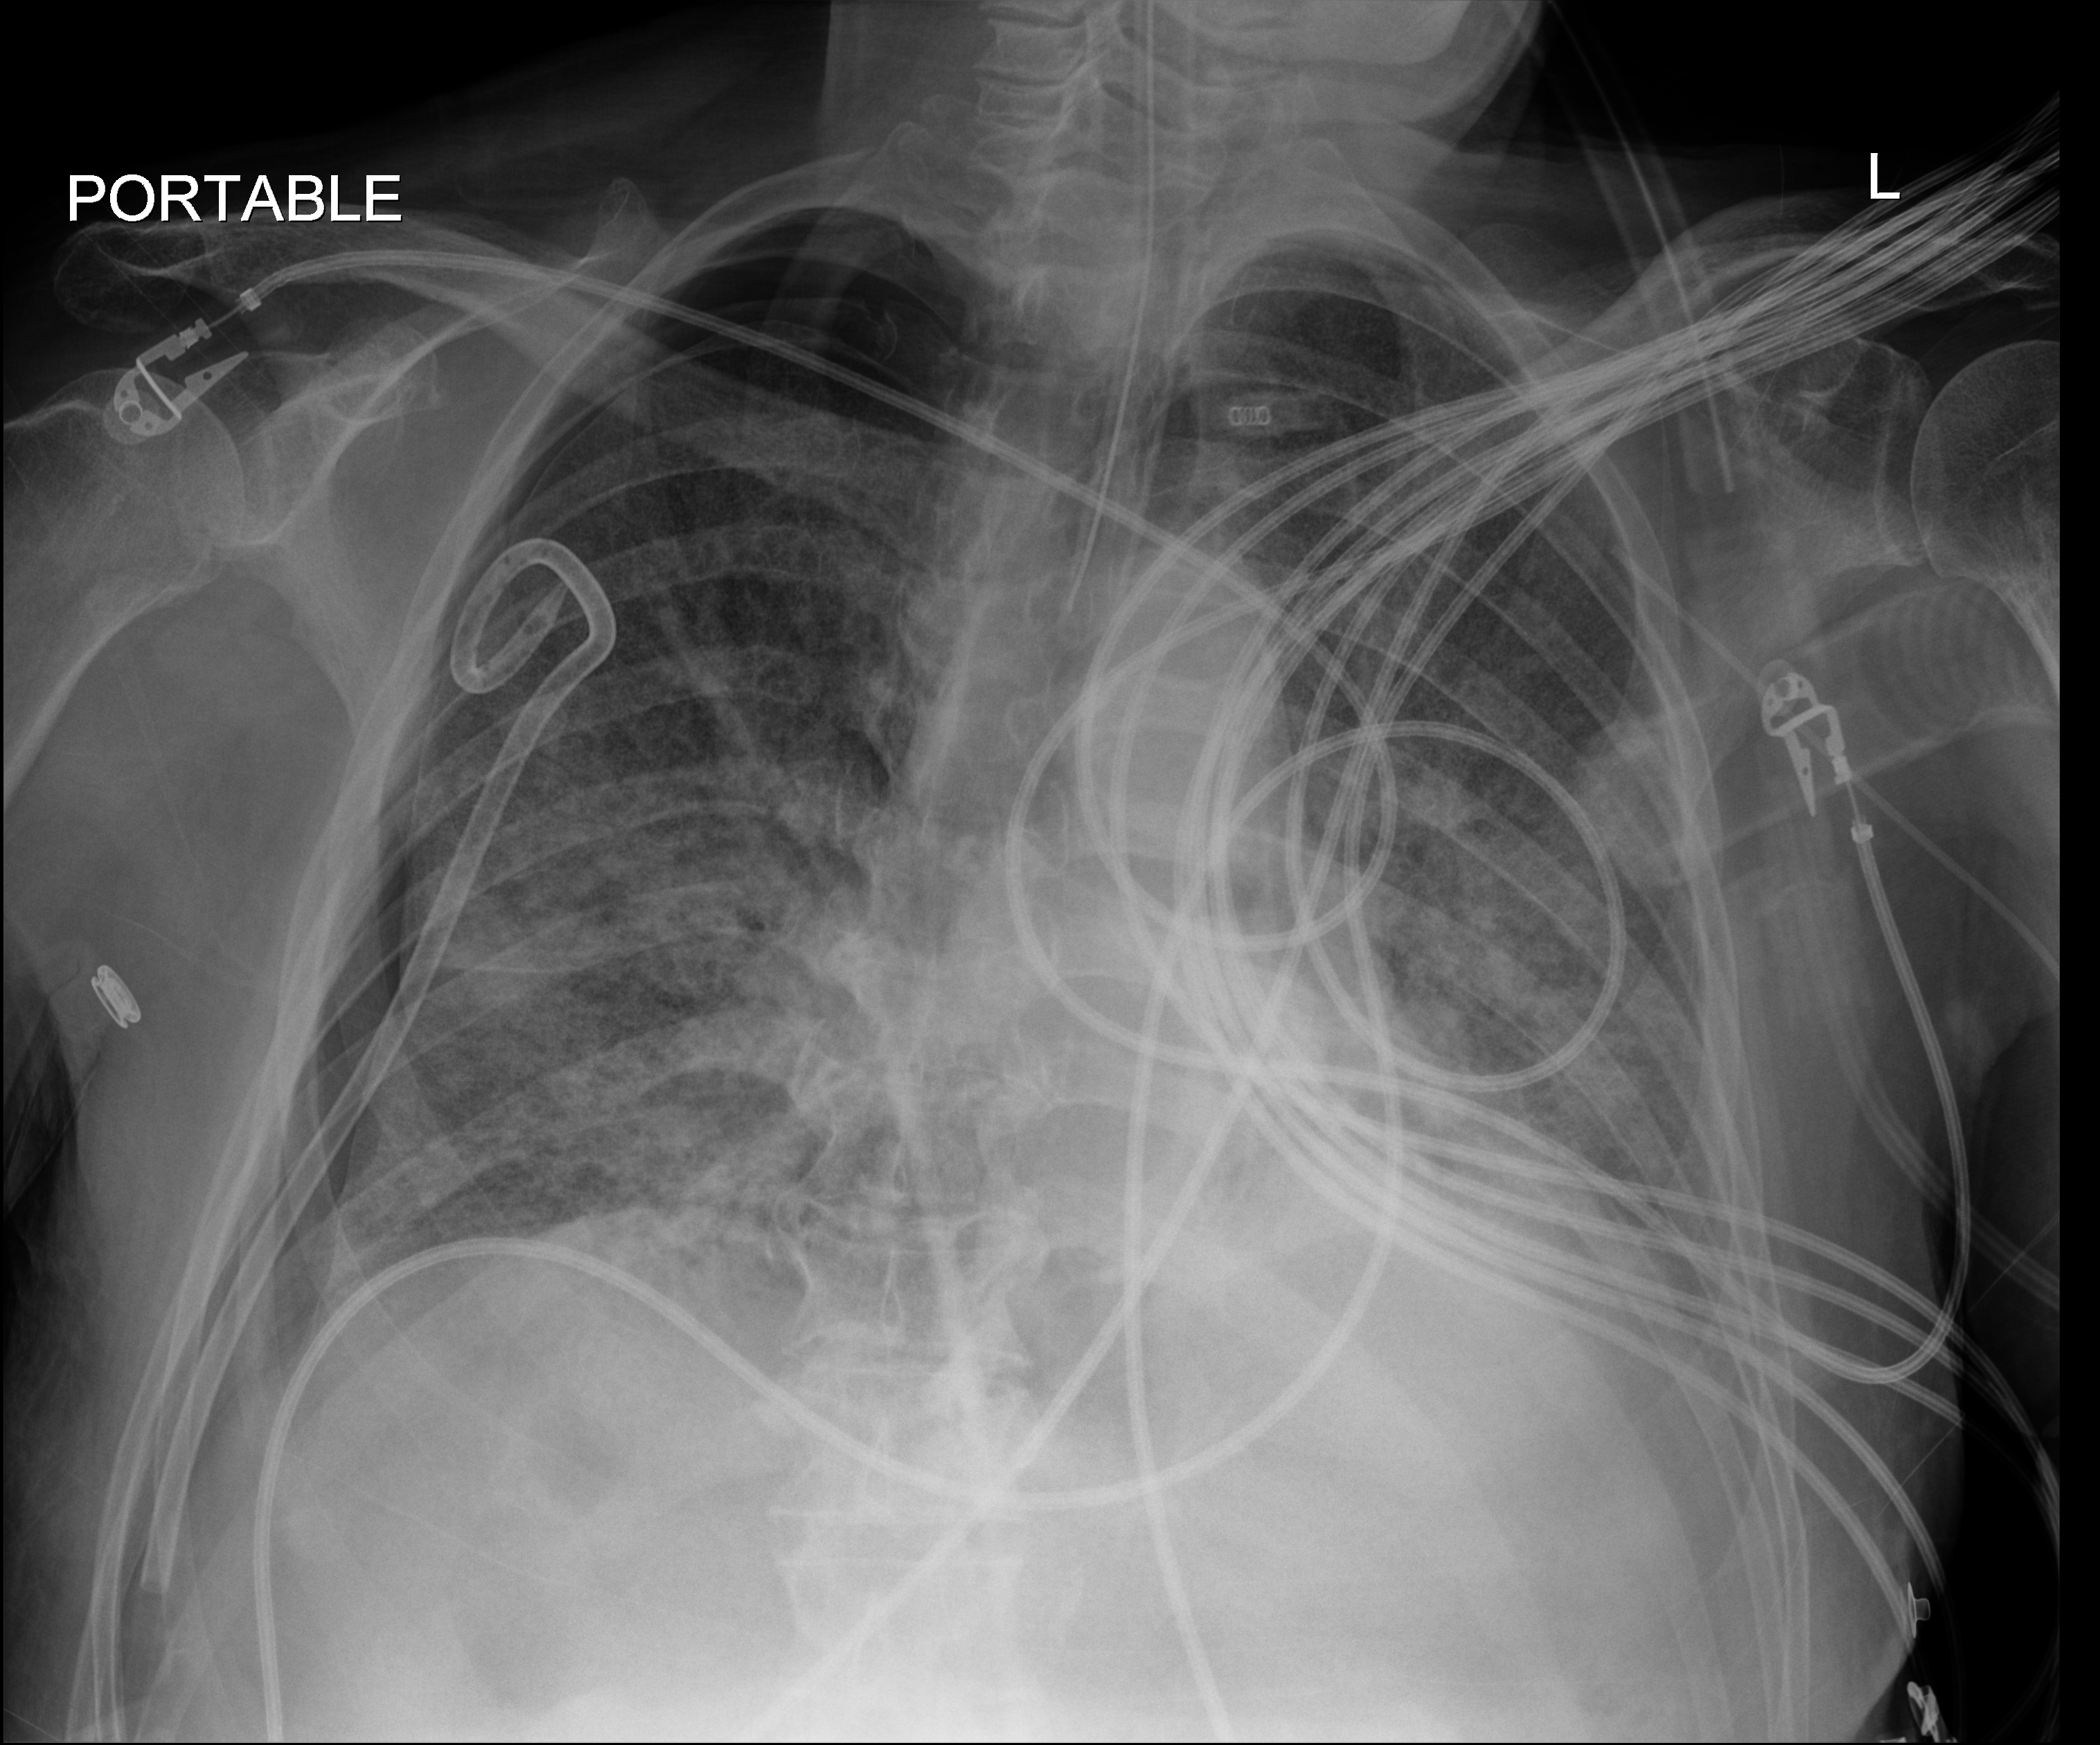
Bedside chest radiograph (digital radiography). Male patient hospitalised with COVID-19, age 75–90 years.
Admission-level facts for this patient (not findings on this image; timing relative to this image not recorded): mechanically ventilated during this hospital stay: yes.